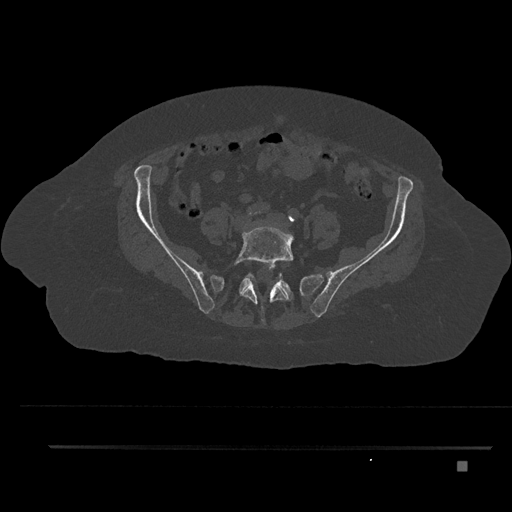
CT including the spine, one axial slice; position 32 of 797 along the scan axis; 120 kVp; bone window (W 1800 / L 400 HU); 0.5 mm slice thickness; 512 × 512 image matrix, field of view 437 × 437 mm. Female patient, age 76 years. Case-level facts recorded for this patient, not image findings: primary cancer: lung; vertebrae with lytic lesions (as recorded): T11, L3.
Outlined on this slice (semi-automatic segmentation, software-assisted and operator-edited):
- L5 vertebra: box from (x=234, y=224) to (x=295, y=323) px